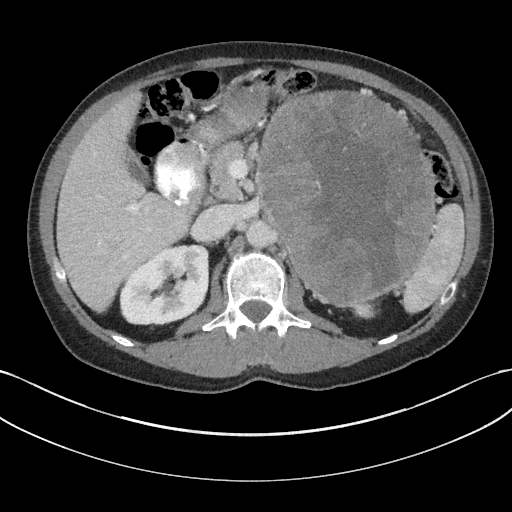
Contrast-enhanced abdominal CT, one axial slice. Slice 107 of 147 in the series (ordered by position). Reconstruction kernel I31f/3. 100 kVp. Intravenous contrast given. Soft-tissue window (W 400 / L 40 HU). 3 mm slice thickness. 512 × 512 image matrix. Patient: male, 58 years. Case-level facts recorded for this patient, not image findings: diagnosis: adrenocortical carcinoma; tumour side: left adrenal; tumour size at pathology: 22 cm.
Annotated regions visible in this slice (semi-automatically segmented with operator editing):
- mass: bounding box (x1, y1, x2, y2) in pixels: (262, 93, 431, 301)